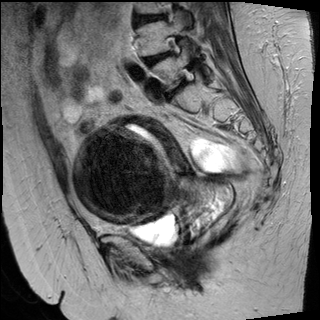
Pelvic MRI for cervical cancer, one sagittal slice; position 22 of 50 along the scan axis; T2-weighted; 1.5 T; TE 89 ms, TR 4880 ms; 4 mm slice thickness; 320 × 320 image matrix, field of view 260 × 260 mm. Patient: female, 50 years.
Structures marked on this image (expert manual segmentation):
- uterus and cervix: box from (x=72, y=117) to (x=234, y=234) px